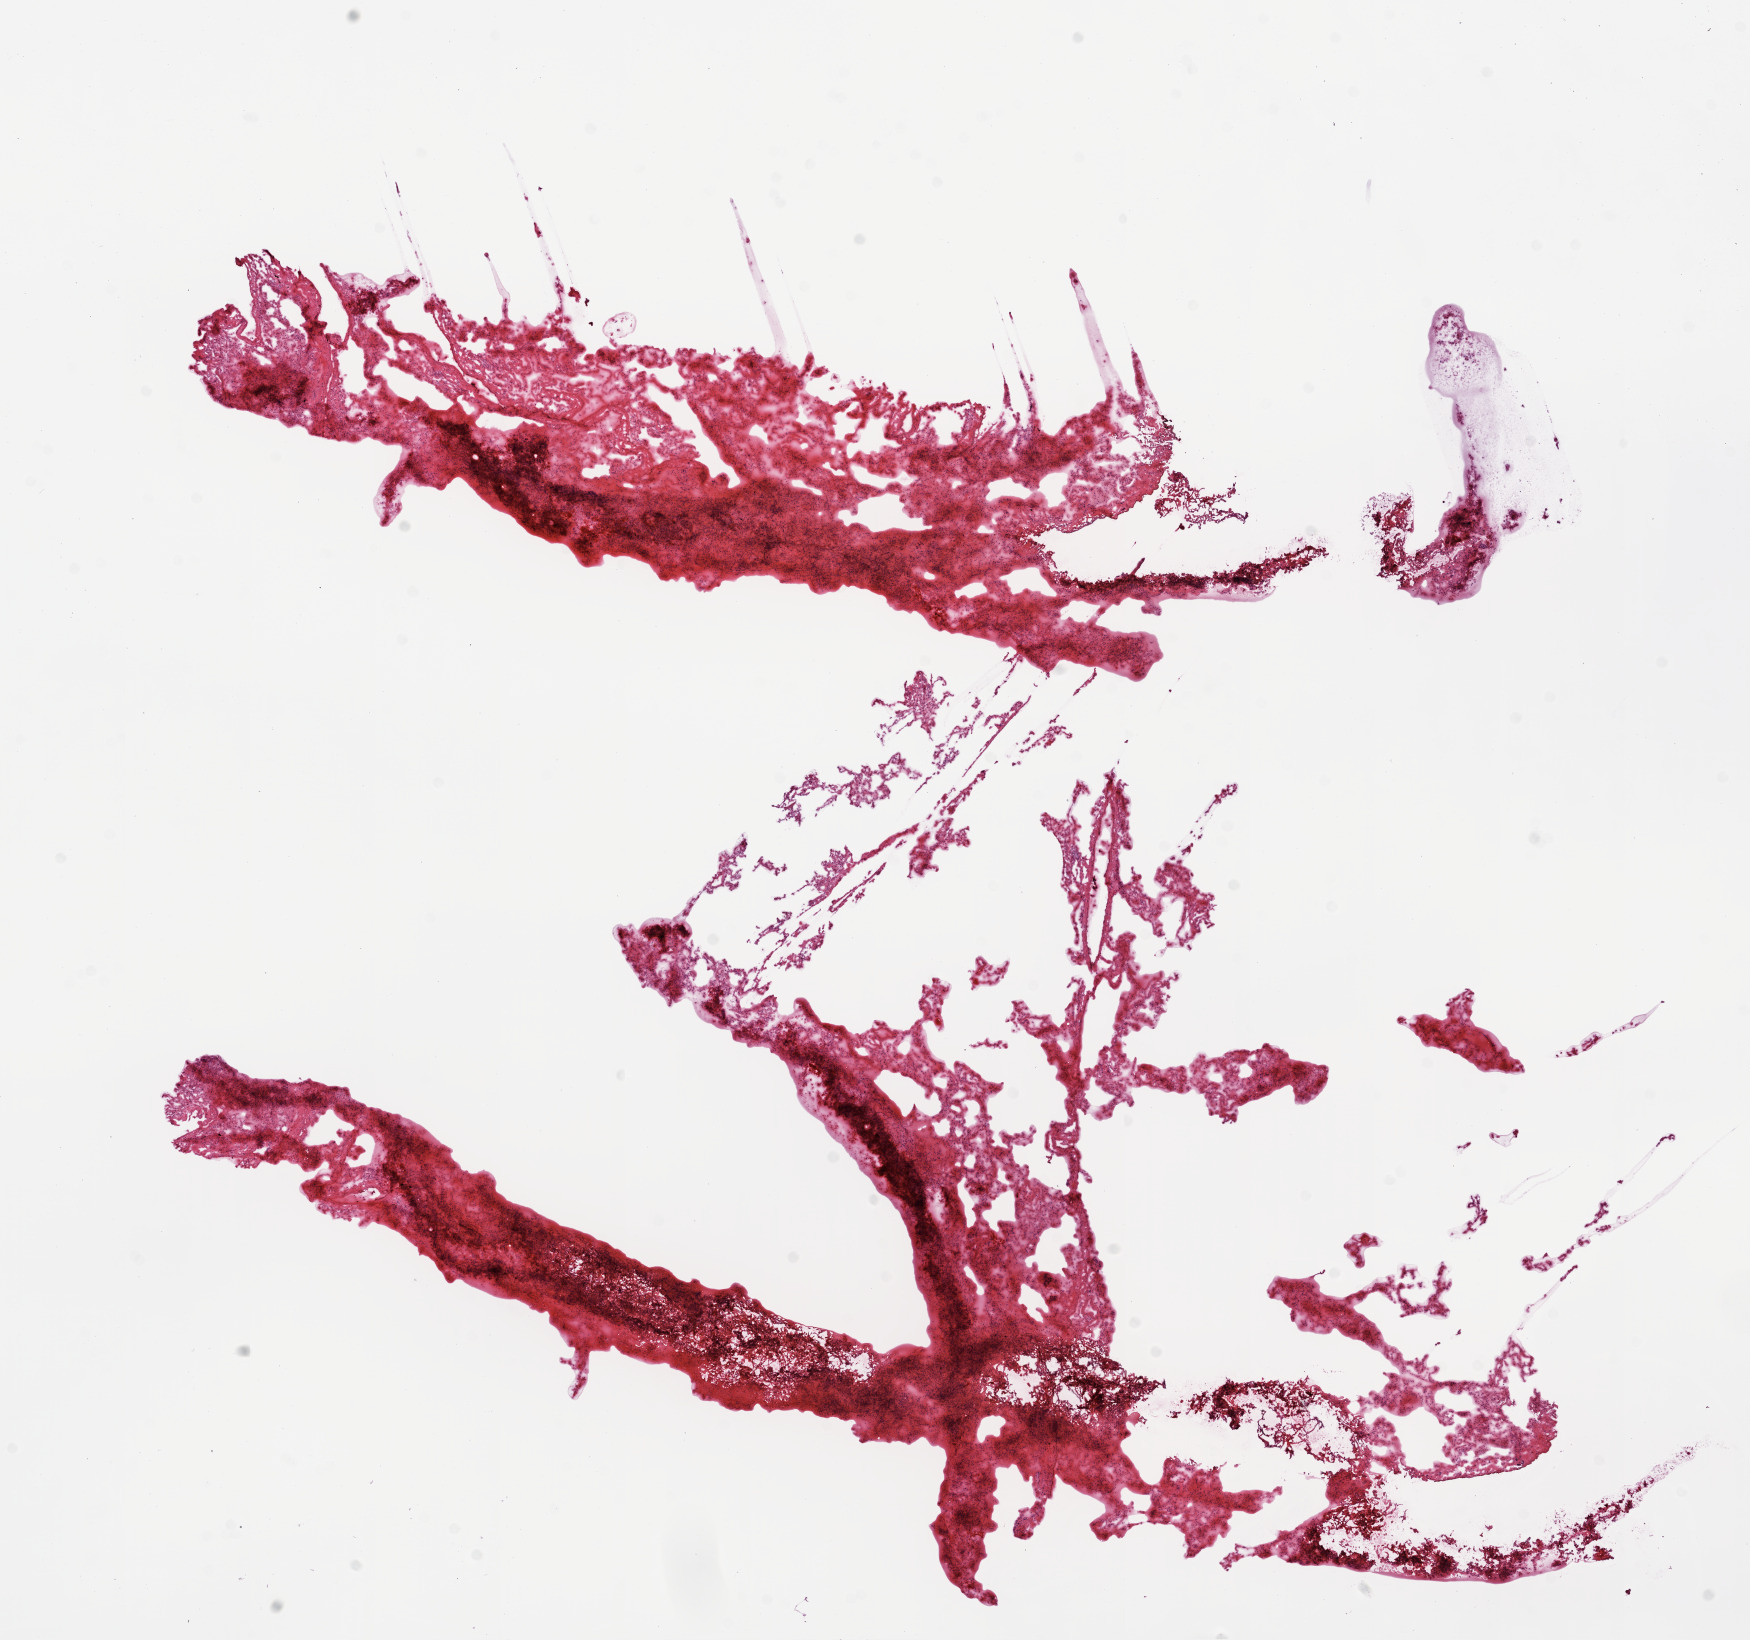
Digitized Hematoxylin and eosin (H&E) stained tissue section (whole slide) — whole scanned area (about 14.0 x 13.2 mm) shown as a low-resolution overview; frozen section from the bottom of the tissue portion; lung, solid tissue normal (non-tumour tissue) sample. Male, age 59 years at initial diagnosis.
This section: solid tissue normal (non-tumour) sample from the same patient. Patient diagnosis: Adenocarcinoma, NOS (lower lobe, lung).